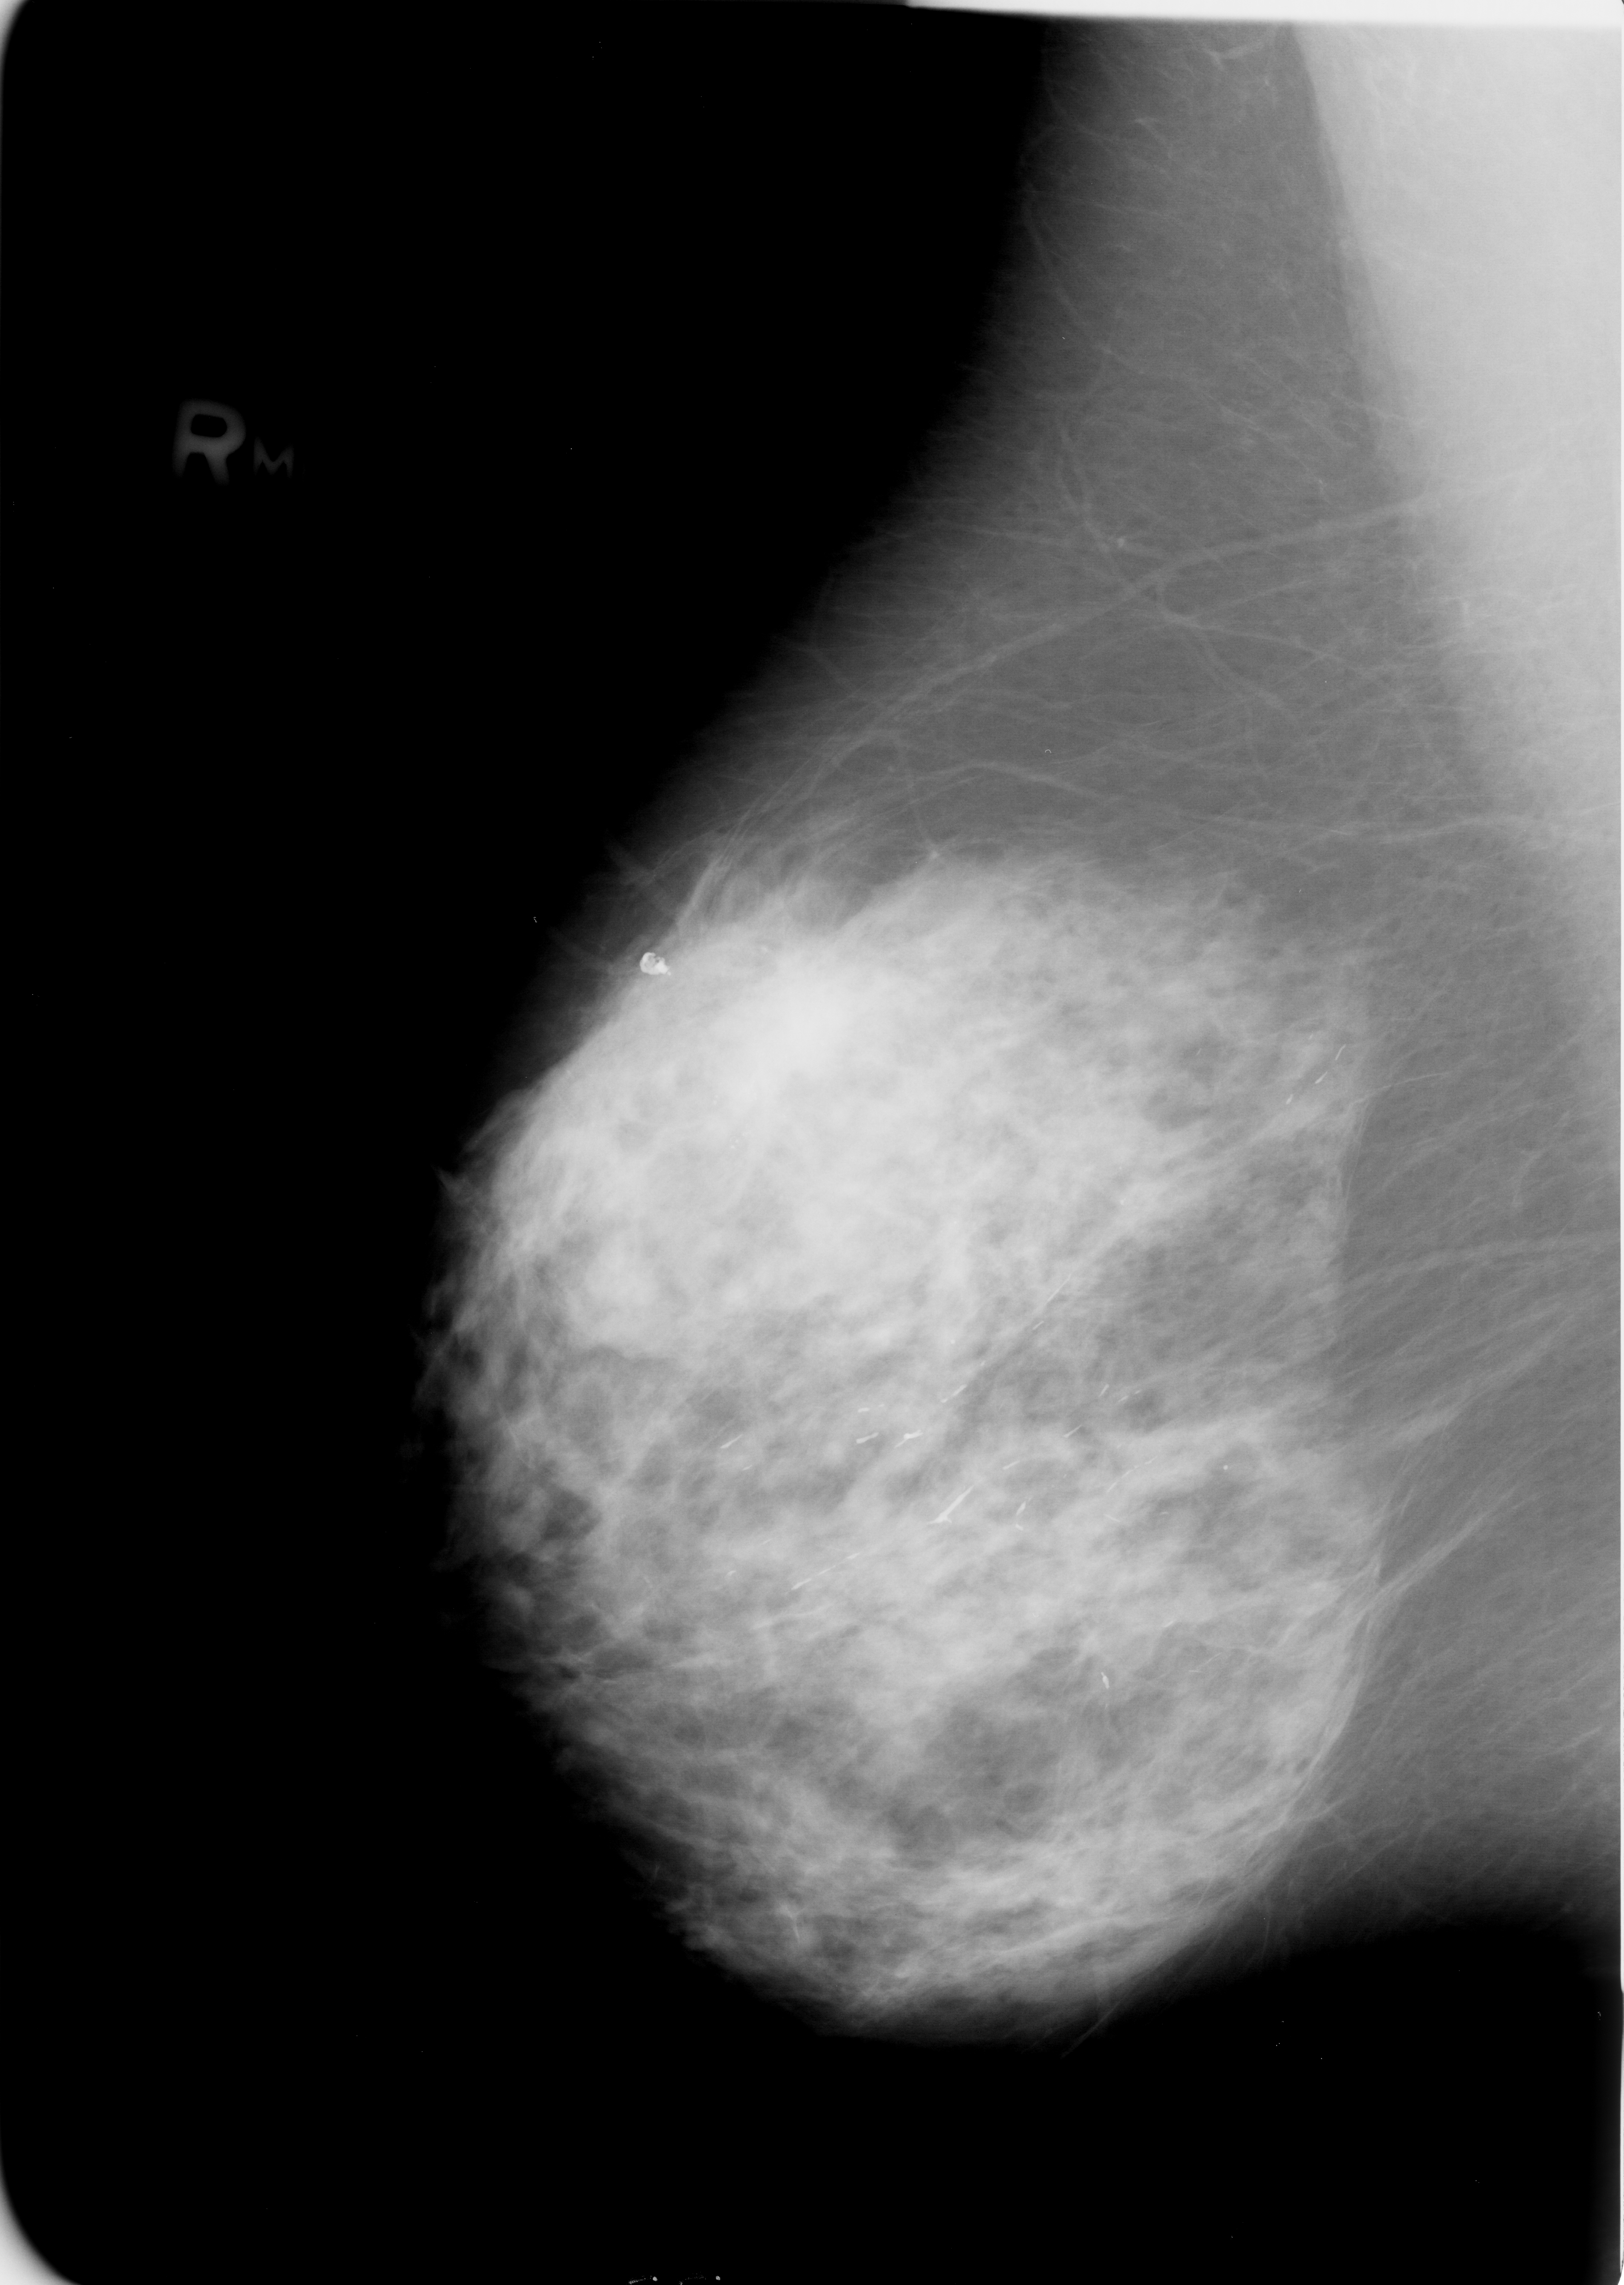
Digitized screen-film mammogram; right breast; MLO view; breast composition: heterogeneously dense (BI-RADS density category 3 of 4).
Radiologist-marked abnormalities on this image: mass, shape irregular / architectural distortion, margins obscured / ill defined / spiculated; BI-RADS assessment category 4; pathology result (as recorded, not read from the image): malignant.